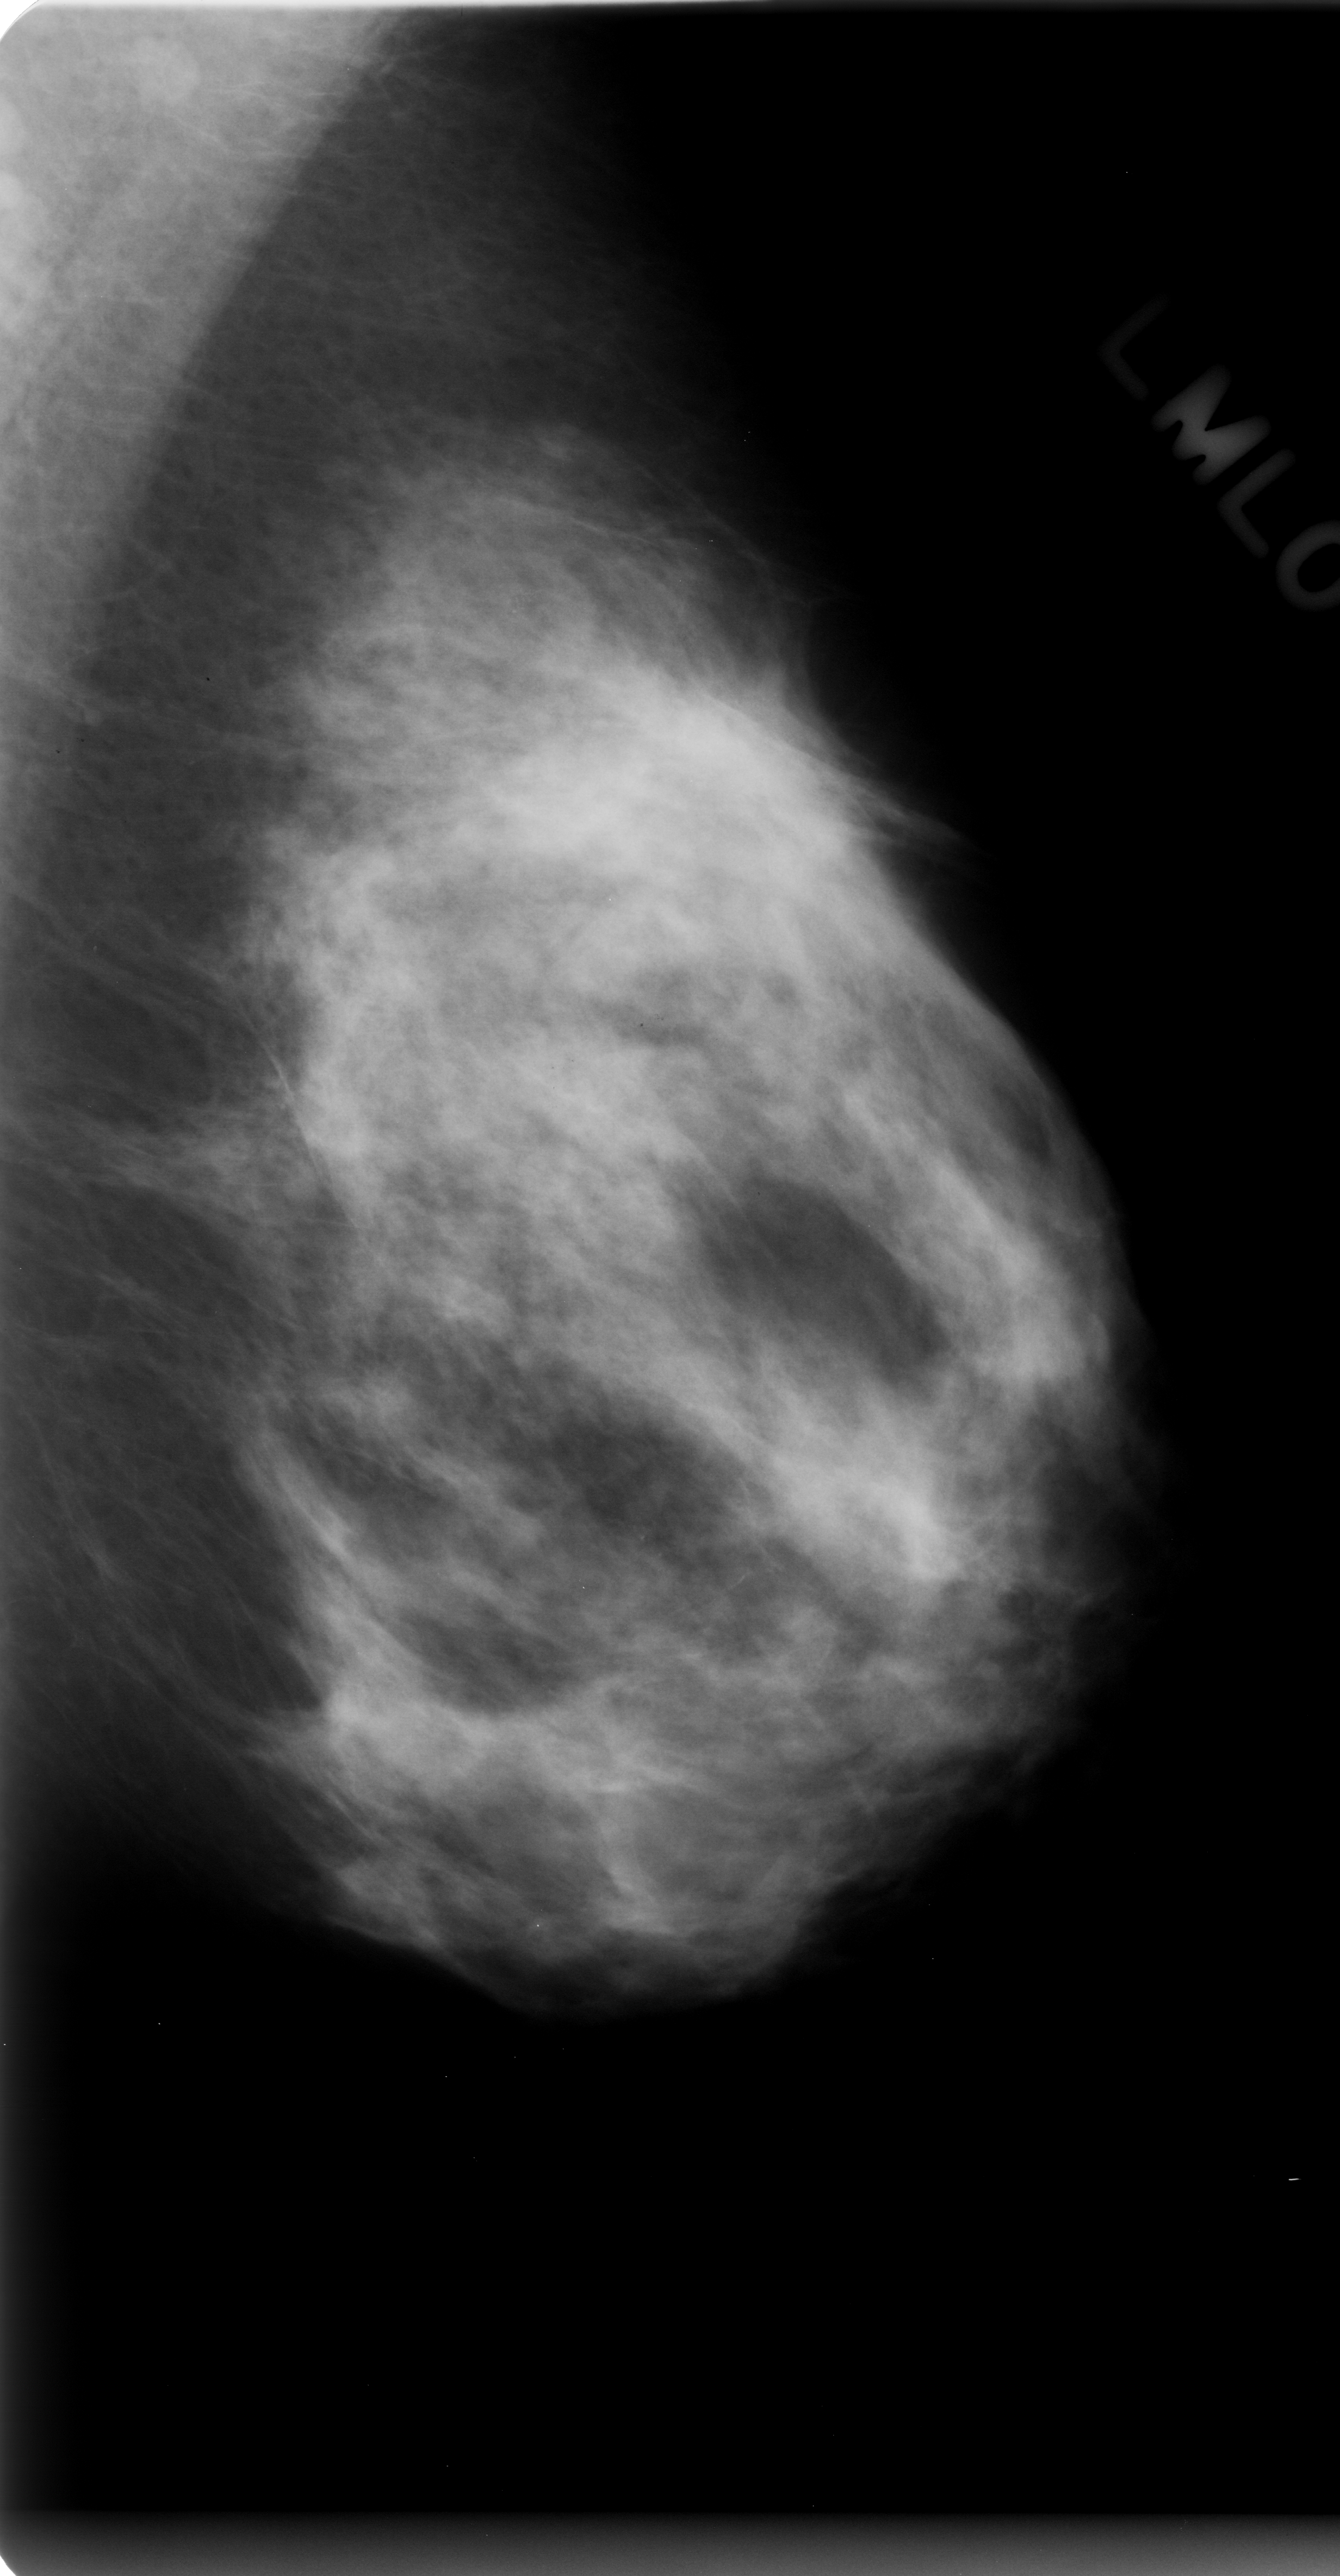
Digitized screen-film mammogram. Left breast. Mediolateral oblique (MLO) view. BI-RADS breast density category 3 (scale 1–4). 1340 × 2576 image matrix.
Expert-marked regions of interest on this film, with their recorded descriptors:
- Finding 1 of 2: calcifications, morphology amorphous, distribution clustered; BI-RADS assessment category 4; pathology result (as recorded, not read from the image): benign: bounding box (x1, y1, x2, y2) in pixels: (400, 483, 610, 702)
- Finding 2 of 2: calcifications, morphology amorphous, distribution clustered; BI-RADS assessment category 4; subtlety rating 1 on a 1 (subtle) to 5 (obvious) scale; pathology result (as recorded, not read from the image): malignant: (522, 1492, 771, 1689)